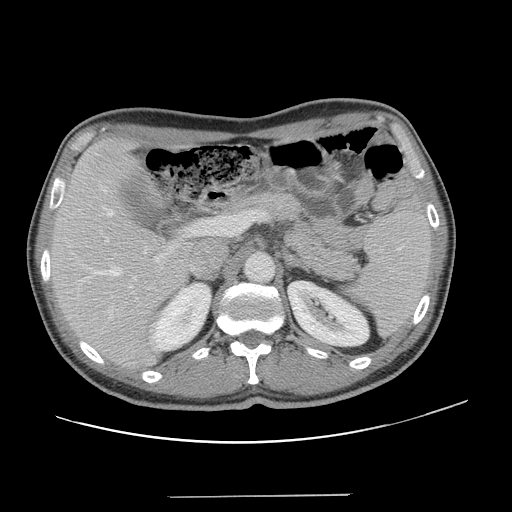
Contrast-enhanced abdominal CT, one axial slice; slice 82 of 131 in the series (ordered by position); 120 kVp; soft-tissue window (W 400 / L 40 HU); 512 × 512 image matrix, field of view 403 × 403 mm. Male patient, age 60 years. Case-level facts recorded for this patient, not image findings: diagnosis: colorectal cancer liver metastases, imaged before liver resection; multiple liver metastases: no; largest metastasis: 2.5 cm; disease in both lobes: no.
Outlined on this slice (manually delineated by an expert):
- hepatic veins: bounding box [x1, y1, x2, y2] px = [94, 187, 146, 313]
- liver: [51, 140, 189, 365]
- planned liver remnant (the part of the liver to remain after resection): [51, 139, 189, 357]
- portal vein (with intrahepatic branches): [106, 220, 214, 288]